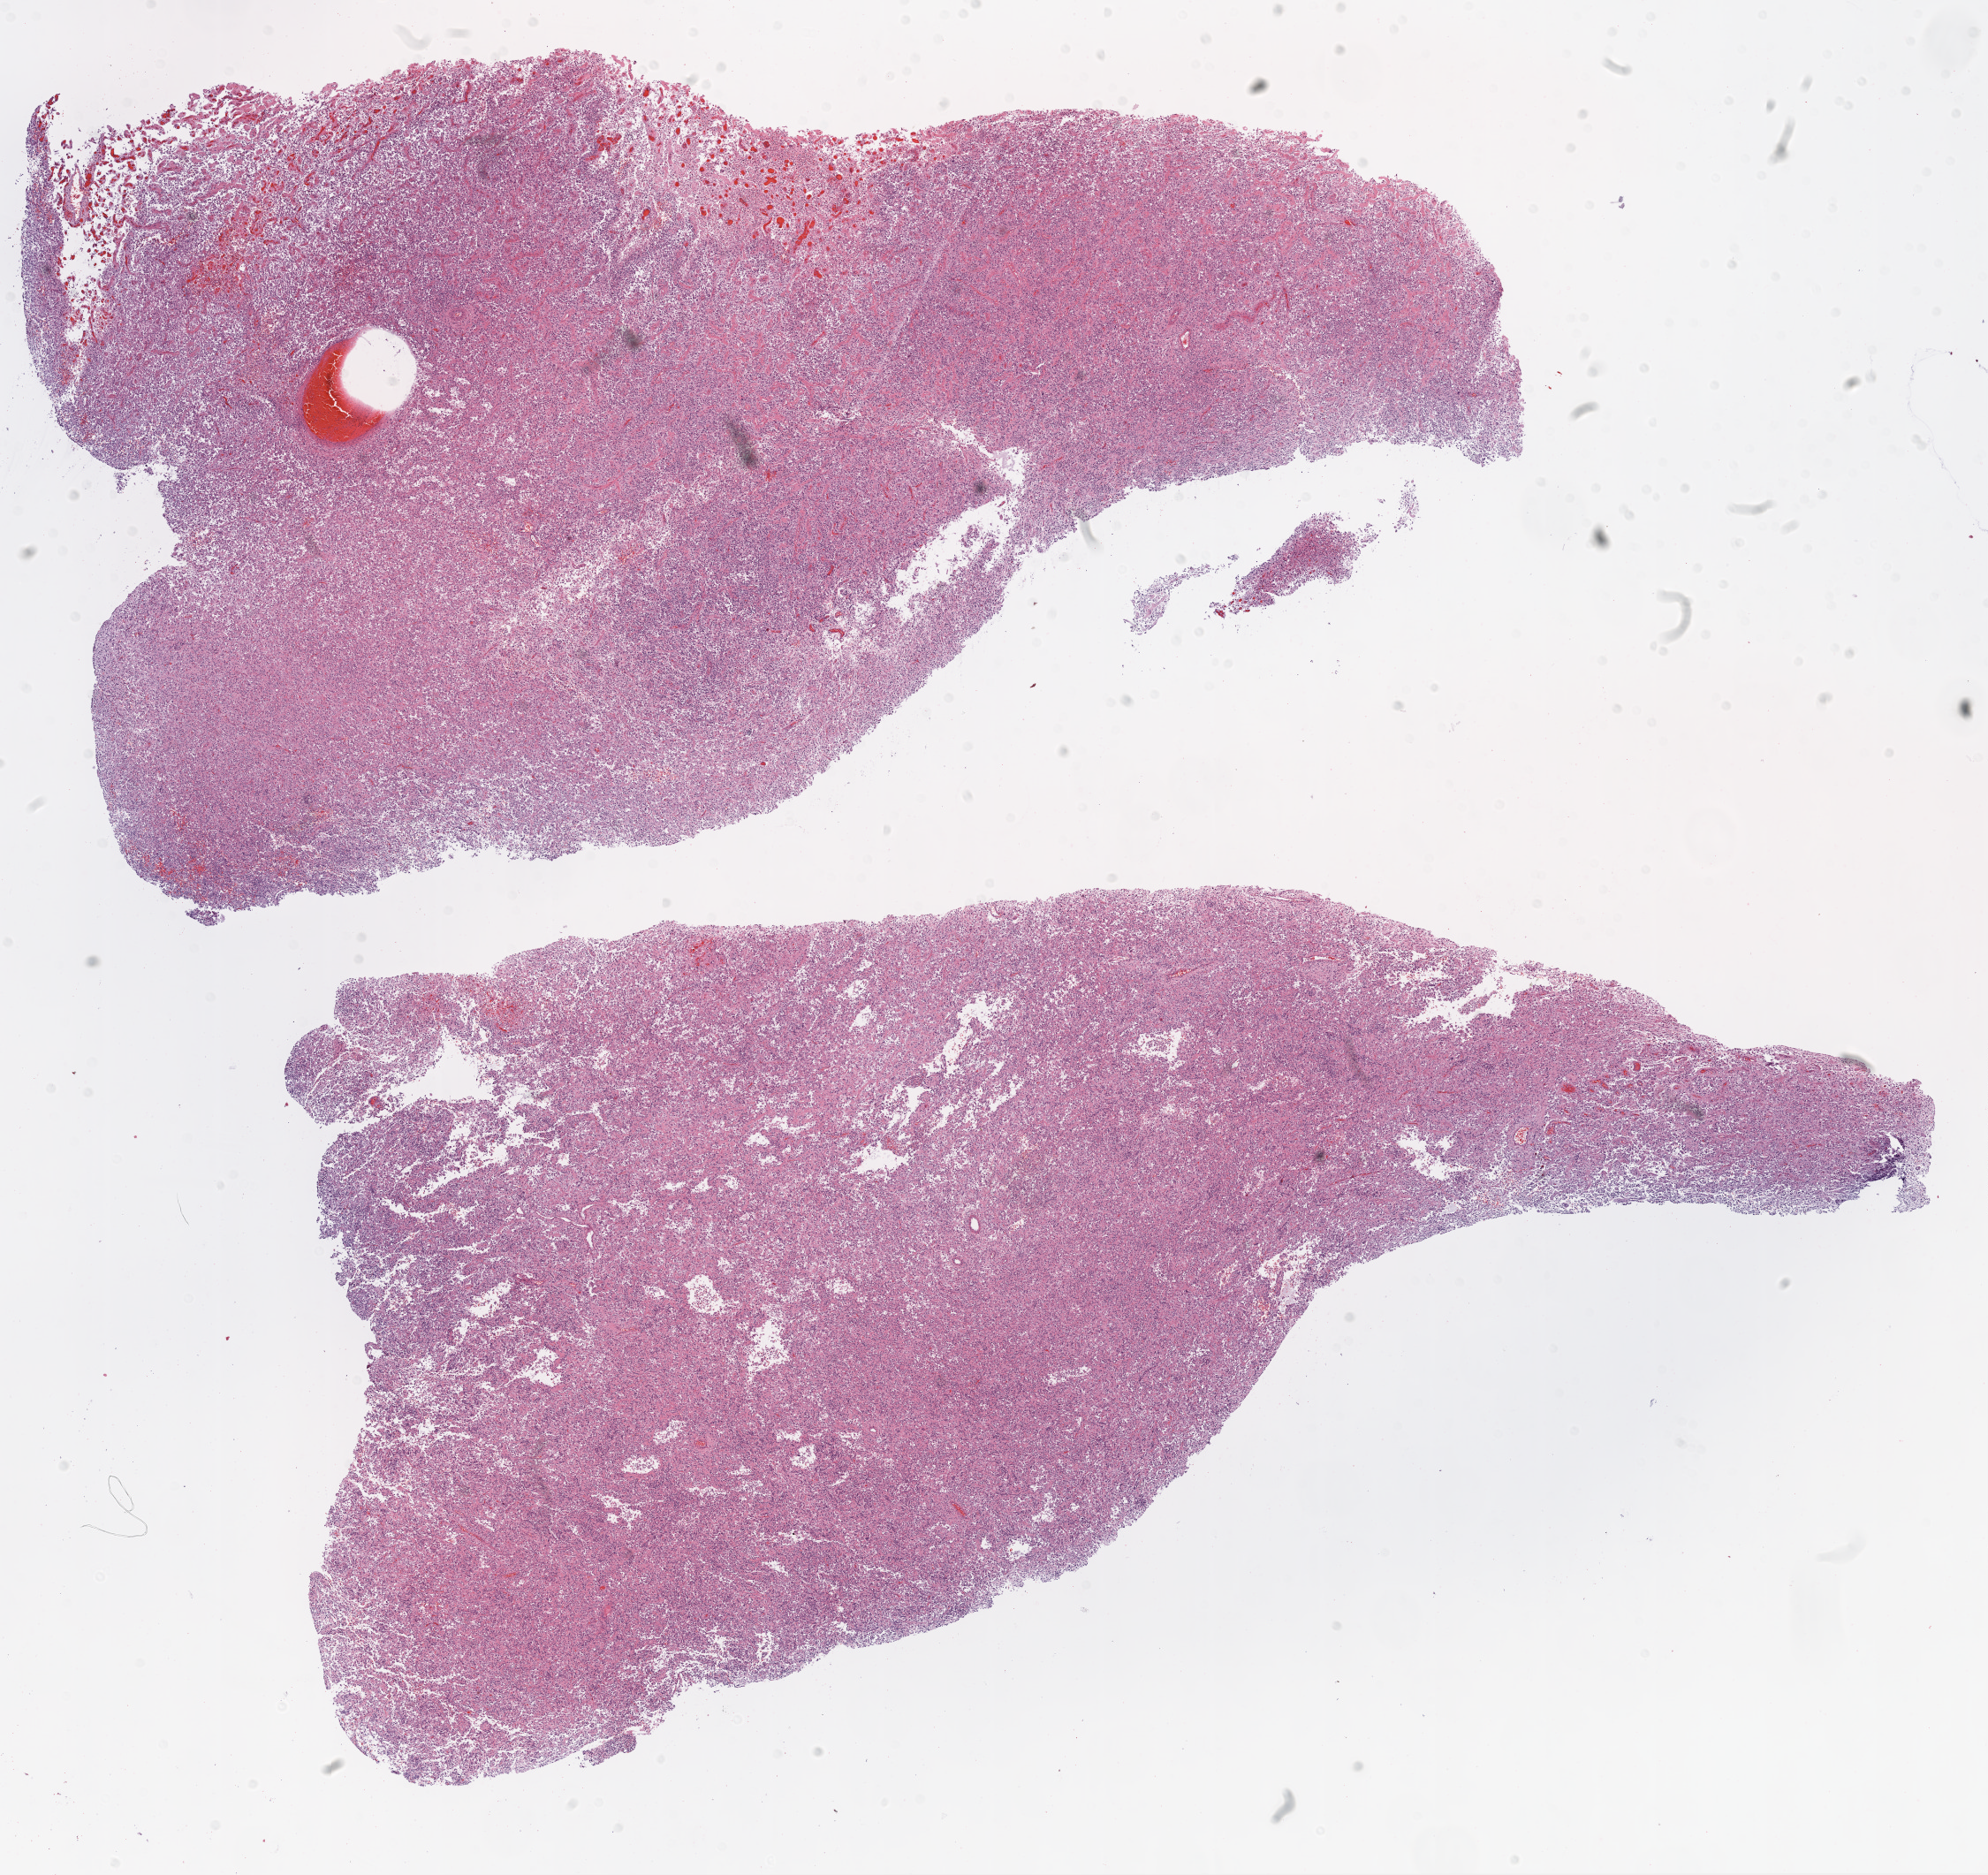
H&E-stained whole-slide image, a low-resolution overview of the entire scanned area, about 18.1 x 17.0 mm (acquisition: 20x scan), formalin-fixed paraffin-embedded (FFPE) diagnostic section, sample: primary tumour, brain. Male patient; age at initial diagnosis 63 years.
Pathologic diagnosis: Glioblastoma.